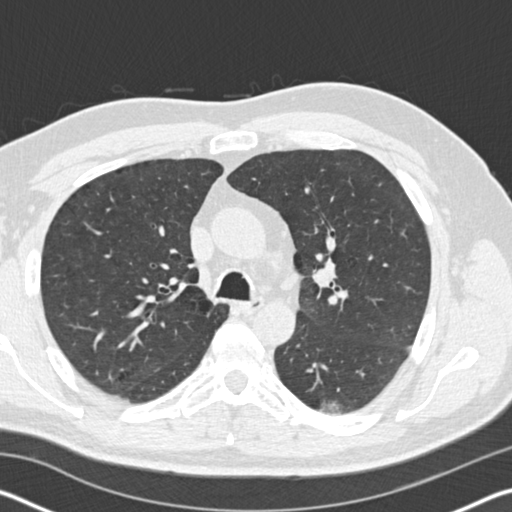
Low-dose screening chest CT, one axial slice. Reconstruction kernel B30f. Lung window (W 1500 / L -600 HU). 2 mm slice thickness. 512 × 512 image matrix.
Structures marked on this image (expert manual segmentation):
- lesion 1 (tumor, lower lobe of left lung): bounding box [x1, y1, x2, y2] px = [322, 402, 341, 414]